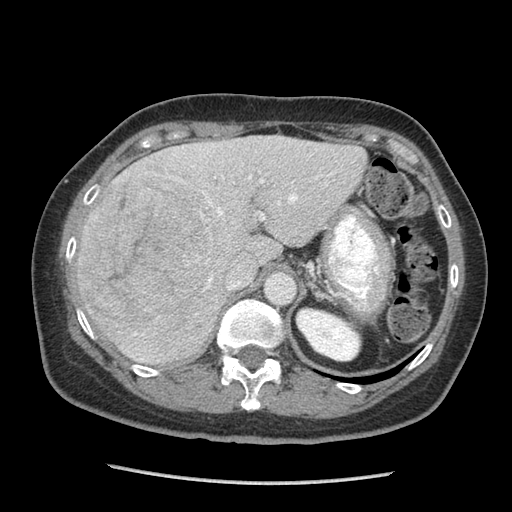
Contrast-enhanced abdominal CT (liver protocol), one axial slice; position 59 of 105 along the scan axis; reconstruction kernel STANDARD; soft-tissue window (W 400 / L 40 HU); 2.5 mm slice thickness; 512 × 512 image matrix, field of view 340 × 340 mm. Case-level facts recorded for this patient, not image findings: diagnosis: hepatocellular carcinoma (patient treated with transarterial chemoembolisation; whether this scan precedes or follows treatment is not stated here); TNM stage (as recorded): Stage-I.
Structures marked on this image (semi-automatic segmentation, software-assisted and operator-edited):
- abdominal aorta: box from (x=266, y=274) to (x=294, y=303) px
- liver parenchyma outside the tumour (the mass and vessels are separate outlines, so this box may not span the whole liver): (x=76, y=136)–(x=366, y=364)
- mass: (x=78, y=179)–(x=218, y=336)
- liver vessels: (x=132, y=144)–(x=332, y=360)